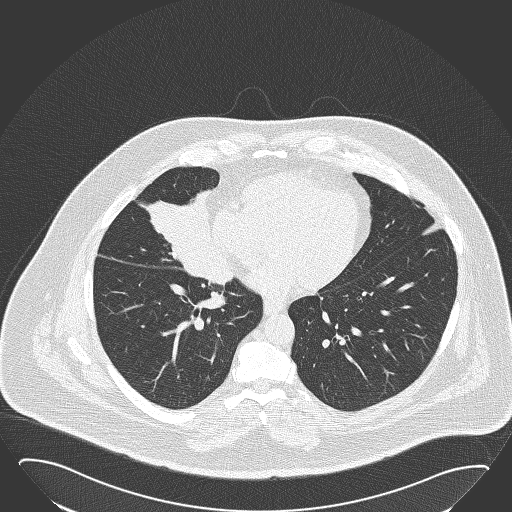
Low-dose screening chest CT, one axial slice. Slice 69 of 168 in the series (ordered by position). Reconstruction kernel B50f. 120 kVp. Lung window (W 1500 / L -600 HU). 2 mm slice thickness. 512 × 512 image matrix, field of view 432 × 432 mm.
Outlined on this slice (expert manual segmentation):
- lesion 1 (tumor, hilum of right lung): bounding box (x1, y1, x2, y2) in pixels: (141, 190, 235, 286)